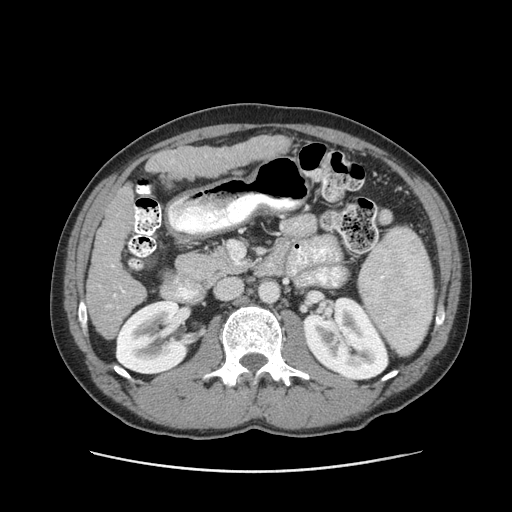
Contrast-enhanced abdominal CT (liver protocol), one axial slice. Slice 37 of 93 in the series (ordered by position). Reconstruction kernel STANDARD. 120 kVp. Soft-tissue window (W 400 / L 40 HU). 2.5 mm slice thickness. 512 × 512 image matrix, field of view 380 × 380 mm. Case-level facts recorded for this patient, not image findings: diagnosis: hepatocellular carcinoma (patient treated with transarterial chemoembolisation; whether this scan precedes or follows treatment is not stated here); TNM stage (as recorded): Stage-II; Child-Pugh class: A; tumour differentiation: moderately differentiated; tumour nodularity: multinodular.
Annotated regions visible in this slice (semi-automatic segmentation, software-assisted and operator-edited):
- liver parenchyma outside the tumour (the mass and vessels are separate outlines, so this box may not span the whole liver): bounding box <86,136,290,338> (left, top, right, bottom; pixels)
- liver vessels: <108,264,125,307>